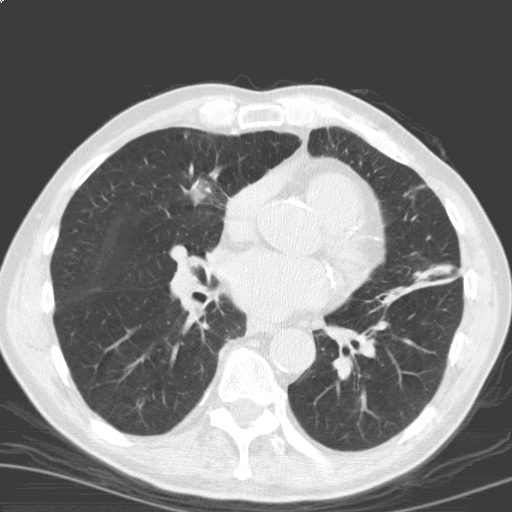
Chest CT (low-dose screening protocol), one axial image; second annual screen; lung window (W 1500 / L -600 HU); 3.2 mm slice thickness; 512 × 512 image matrix, field of view 329 × 329 mm. Male participant, aged 69 years at enrolment. Current smoker at enrolment.
Expert reader's lesion annotation, bounding box <166,157,234,223> (left, top, right, bottom; pixels). The screening reader recorded 2 non-calcified nodules or masses ≥4 mm on this exam (right upper lobe, left lower lobe); which of them this box marks is not recorded. Official screen result: positive, other. Lung cancer was diagnosed 17 days after this screen: squamous cell carcinoma, NOS, right upper lobe, moderately differentiated (G2), stage IB (AJCC 6th edition), 40 mm at pathology.